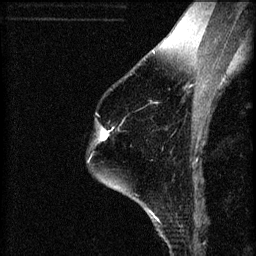
Breast MRI (dynamic contrast-enhanced), one sagittal slice. Slice 45 of 60 in the series (ordered by position). 3 images stored at this slice position (order not interpretable as contrast timing). 1.5 T. TE 4.2 ms, TR 8.2 ms. 256 × 256 image matrix, field of view 180 × 180 mm. Female patient, age 60 years.
Outlined on this slice (semi-automatic segmentation, software-assisted and operator-edited):
- analysis volume of interest (the breast-tissue region the enhancement analysis was run in; not a lesion): bounding box <89,120,114,151> (left, top, right, bottom; pixels)
- tumour enhancement mask (voxels above the 70 % enhancement threshold inside the analysis volume of interest): <101,128,114,141>